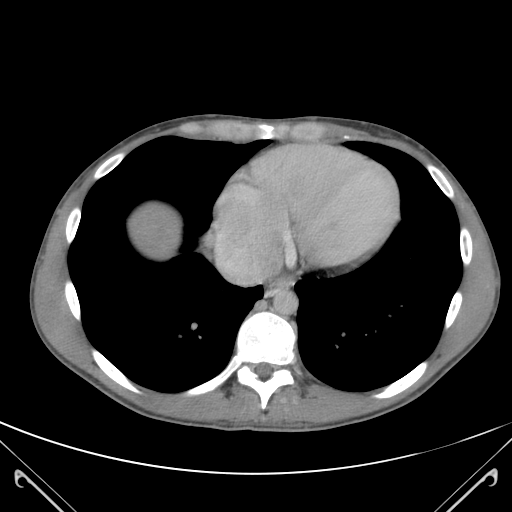
Contrast-enhanced abdominal CT (liver protocol), one axial slice. Position 111 of 118 along the scan axis. 120 kVp. Soft-tissue window (W 400 / L 40 HU). 512 × 512 image matrix. Case-level facts recorded for this patient, not image findings: diagnosis: hepatocellular carcinoma (patient treated with transarterial chemoembolisation; whether this scan precedes or follows treatment is not stated here); TNM stage (as recorded): Stage-IIIB; Child-Pugh class: A; tumour nodularity: uninodular.
Outlined on this slice (semi-automatically segmented with operator editing):
- abdominal aorta: bounding box [x1, y1, x2, y2] px = [274, 291, 298, 314]